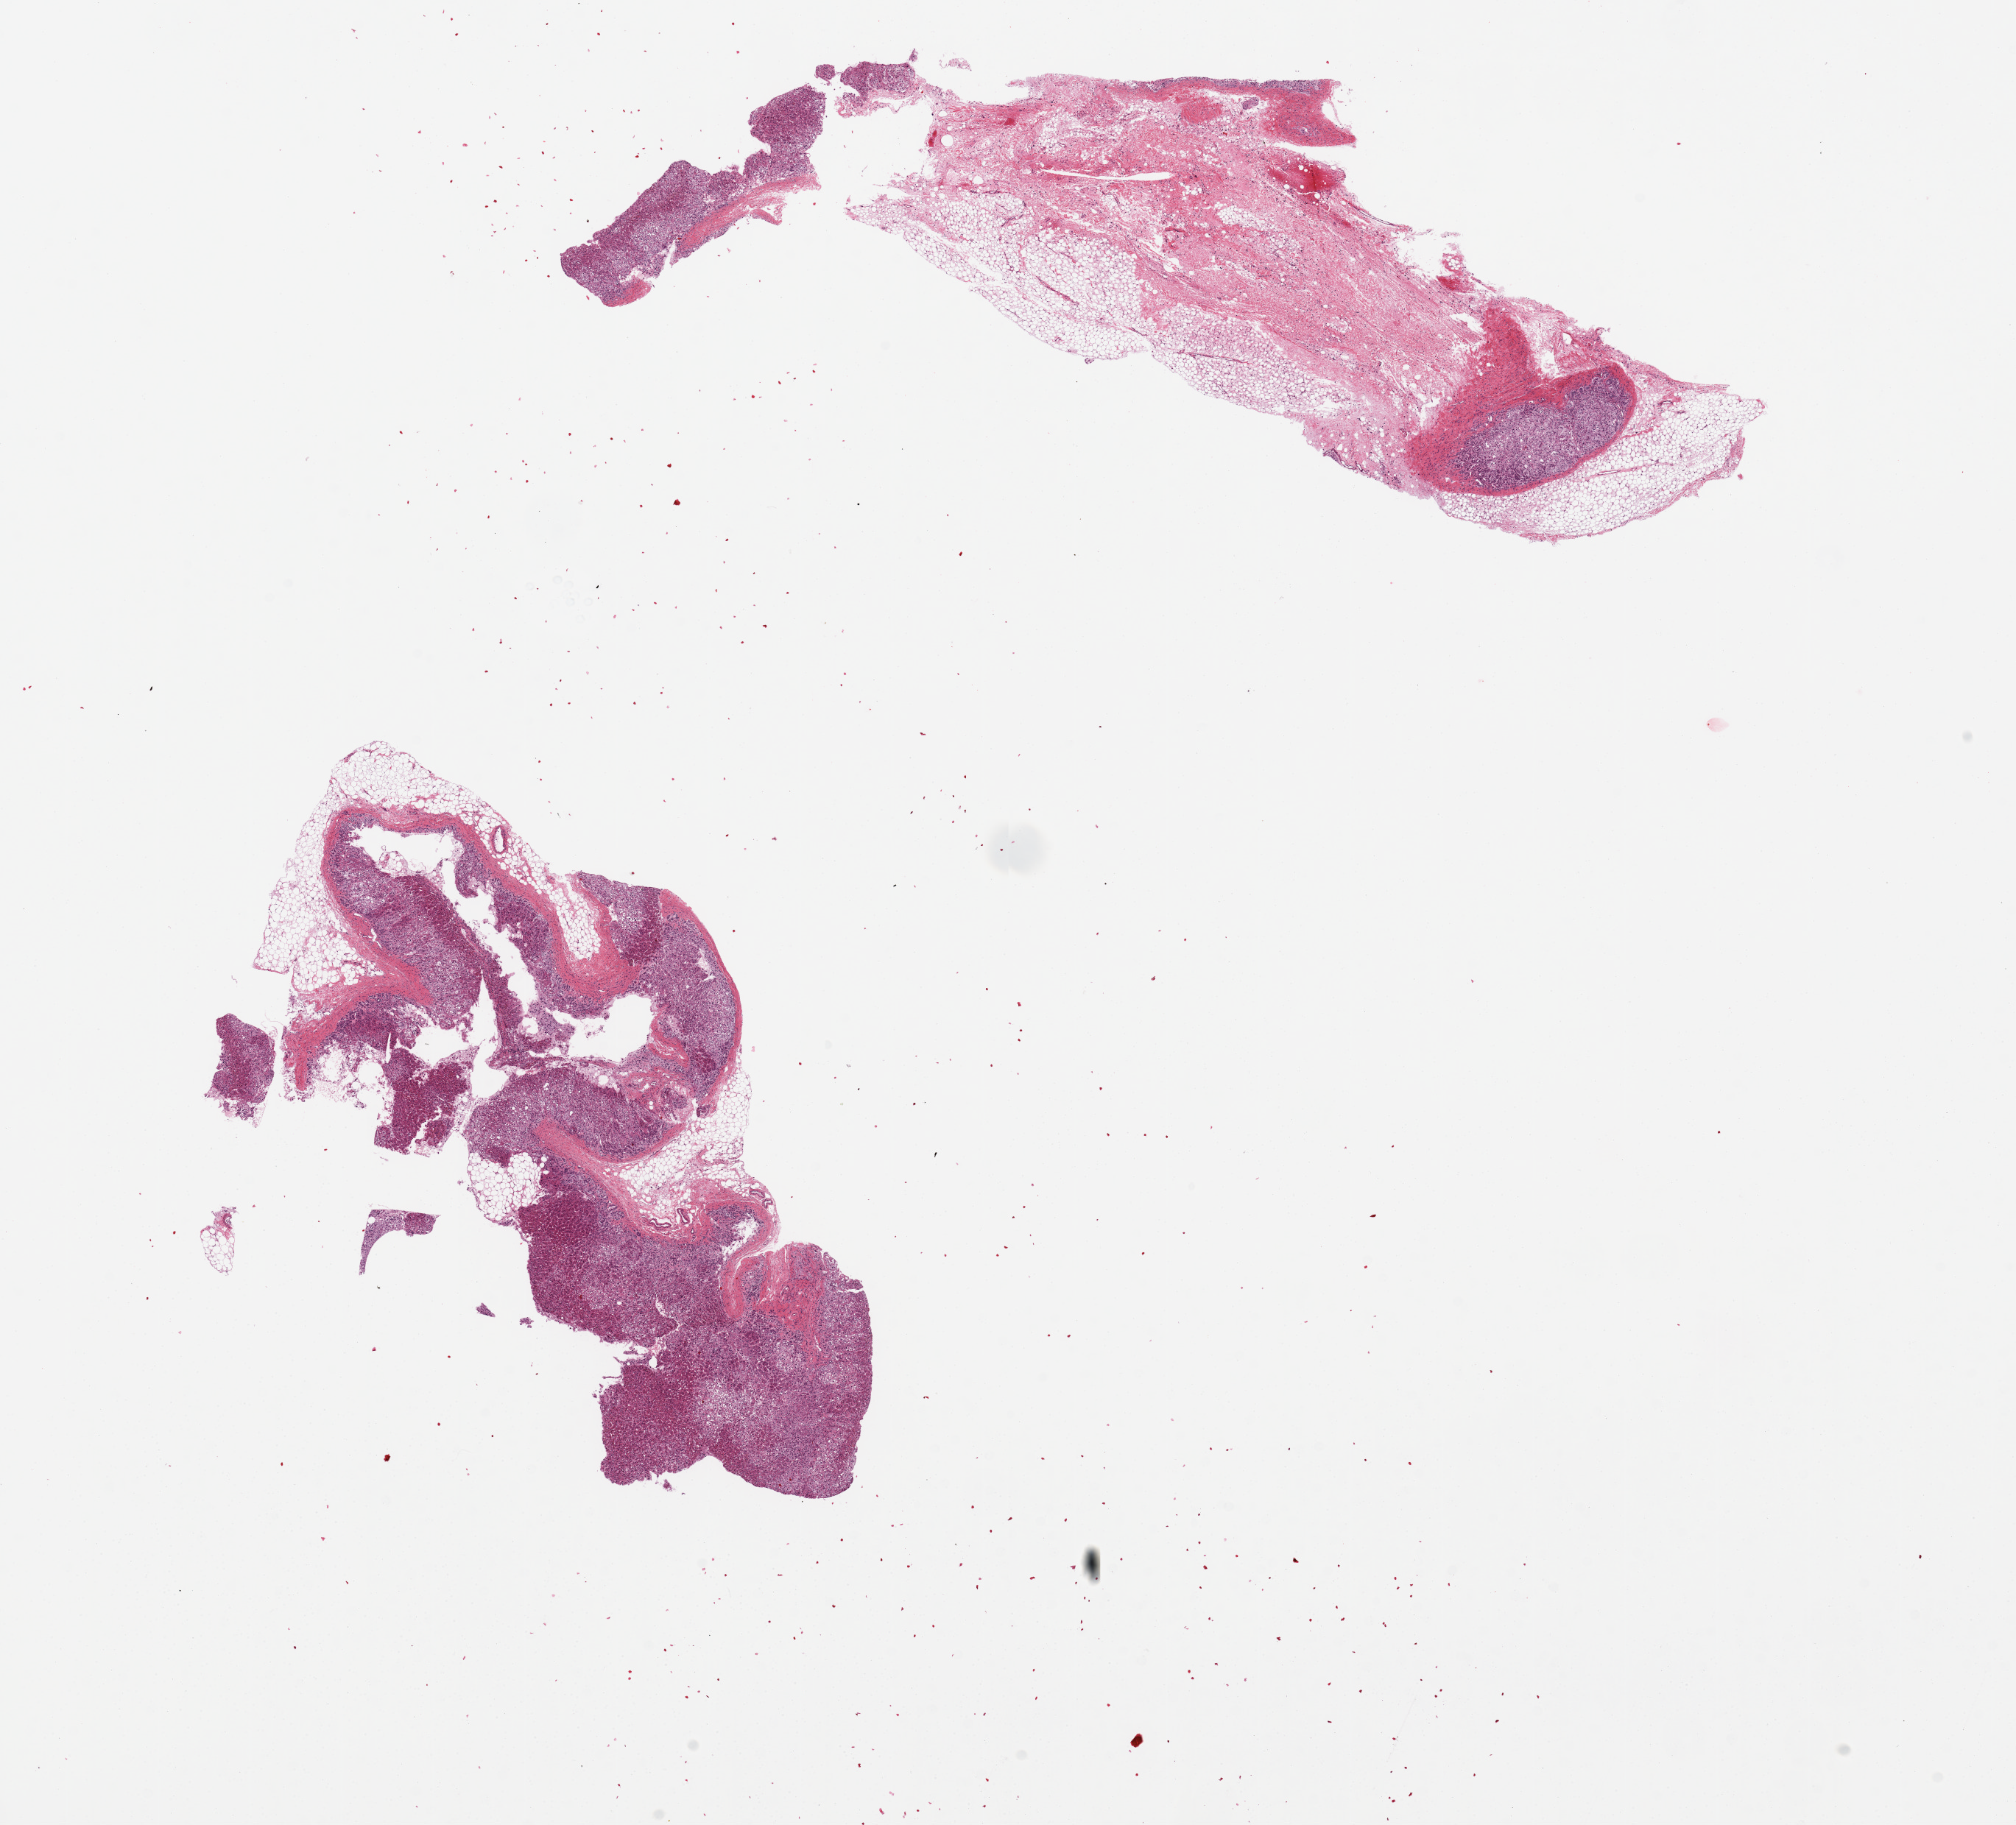
Whole-slide image, H&E stain — a low-resolution overview of the entire scanned area, about 21.7 x 19.6 mm (from a 20x scan), PAXgene-fixed, paraffin-embedded tissue, section of adrenal gland (target tissue), donor tissue sample. Donor: female.
Review note (as recorded): 2 pieces: sample blindly with care: one aliquot is ~20% cortex, rest fat; other is 90% cortex, well preserved.